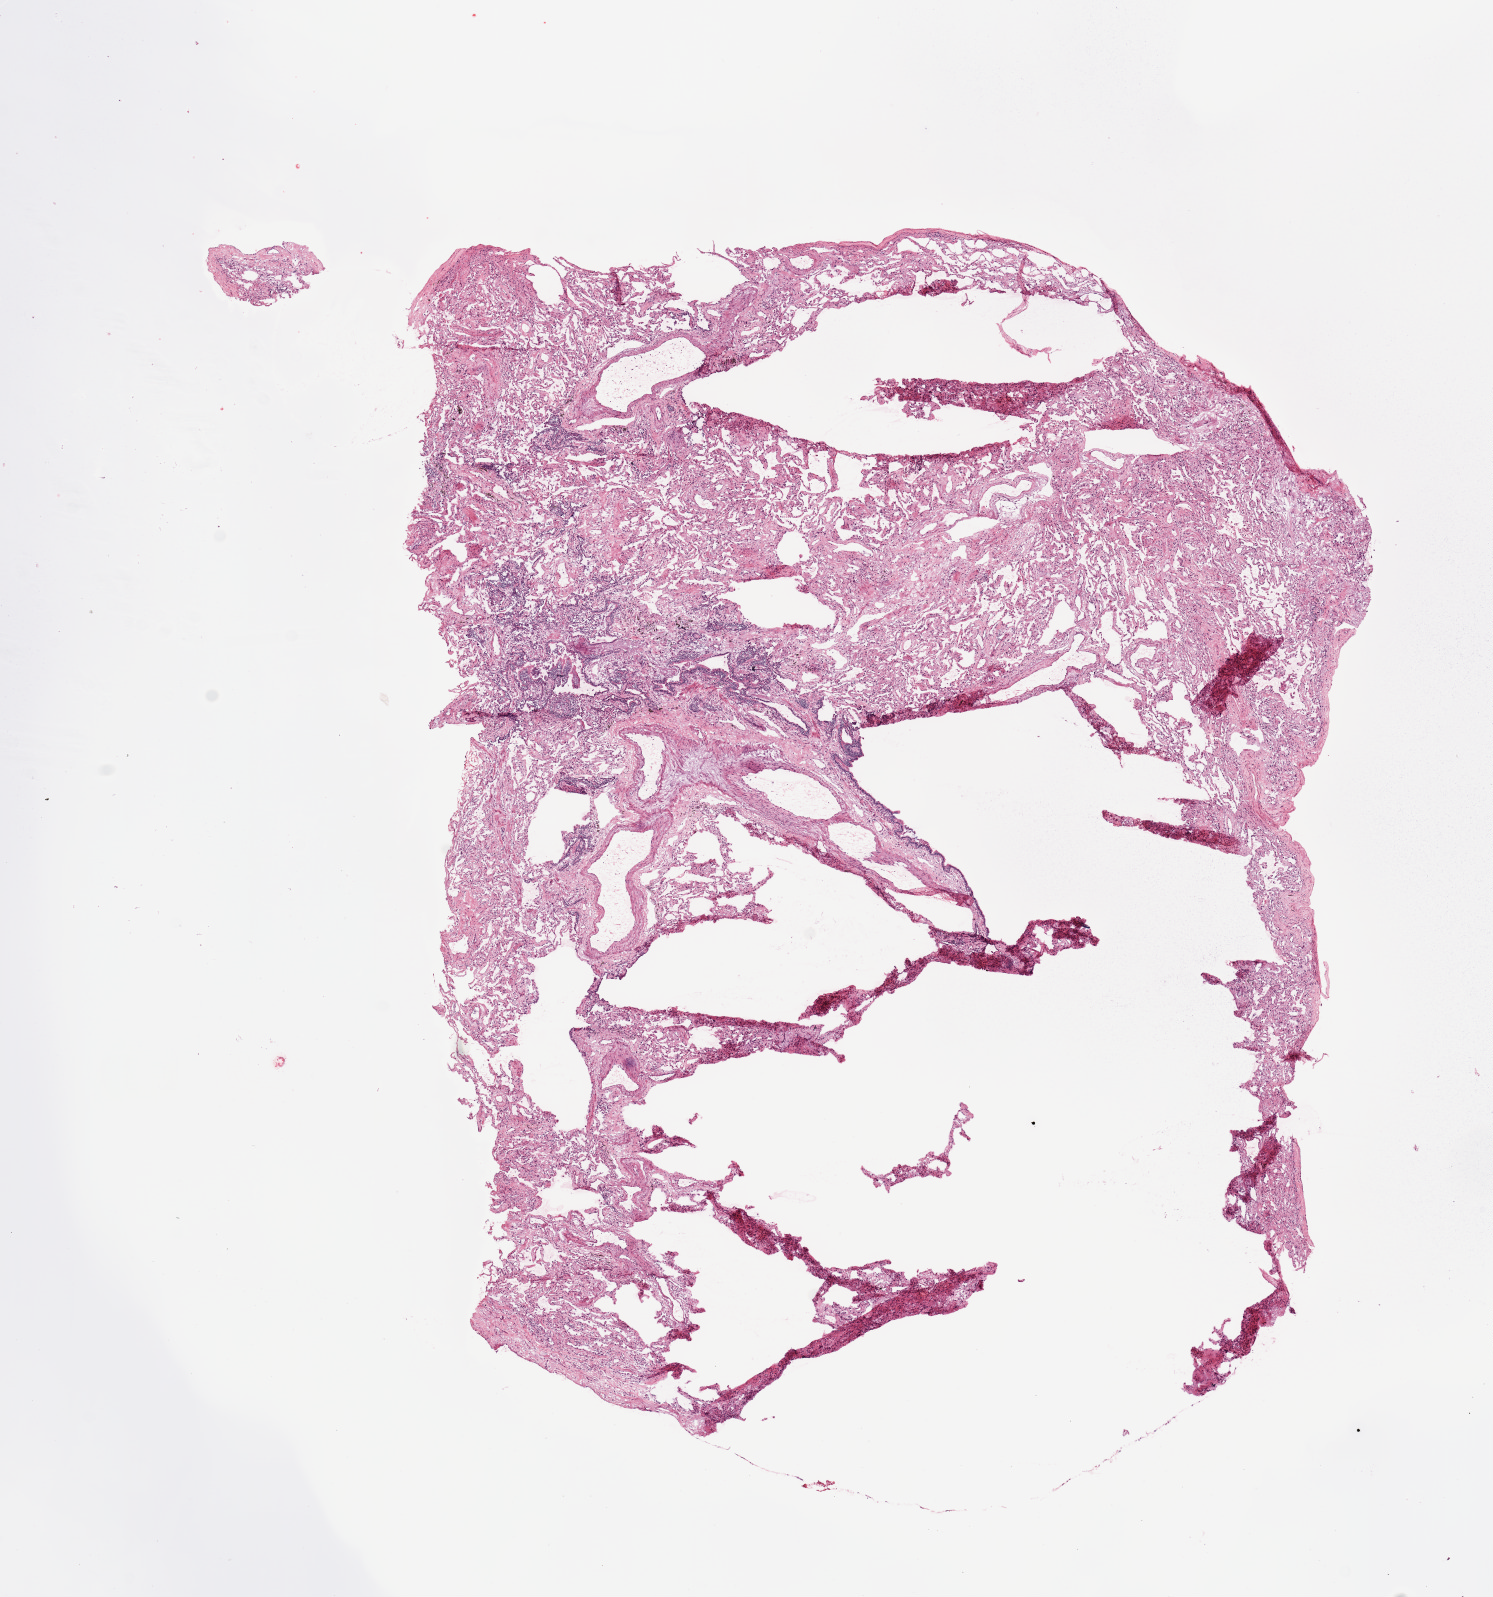
Whole-slide histology image, Hematoxylin and eosin (H&E) stained — a low-resolution overview of the entire scanned area, about 11.8 x 12.6 mm, lung, normal (non-tumour) tissue. Female, 80 y/o.
- this section: normal (non-tumour) tissue from the same patient
- patient diagnosis: Adenocarcinoma, NOS